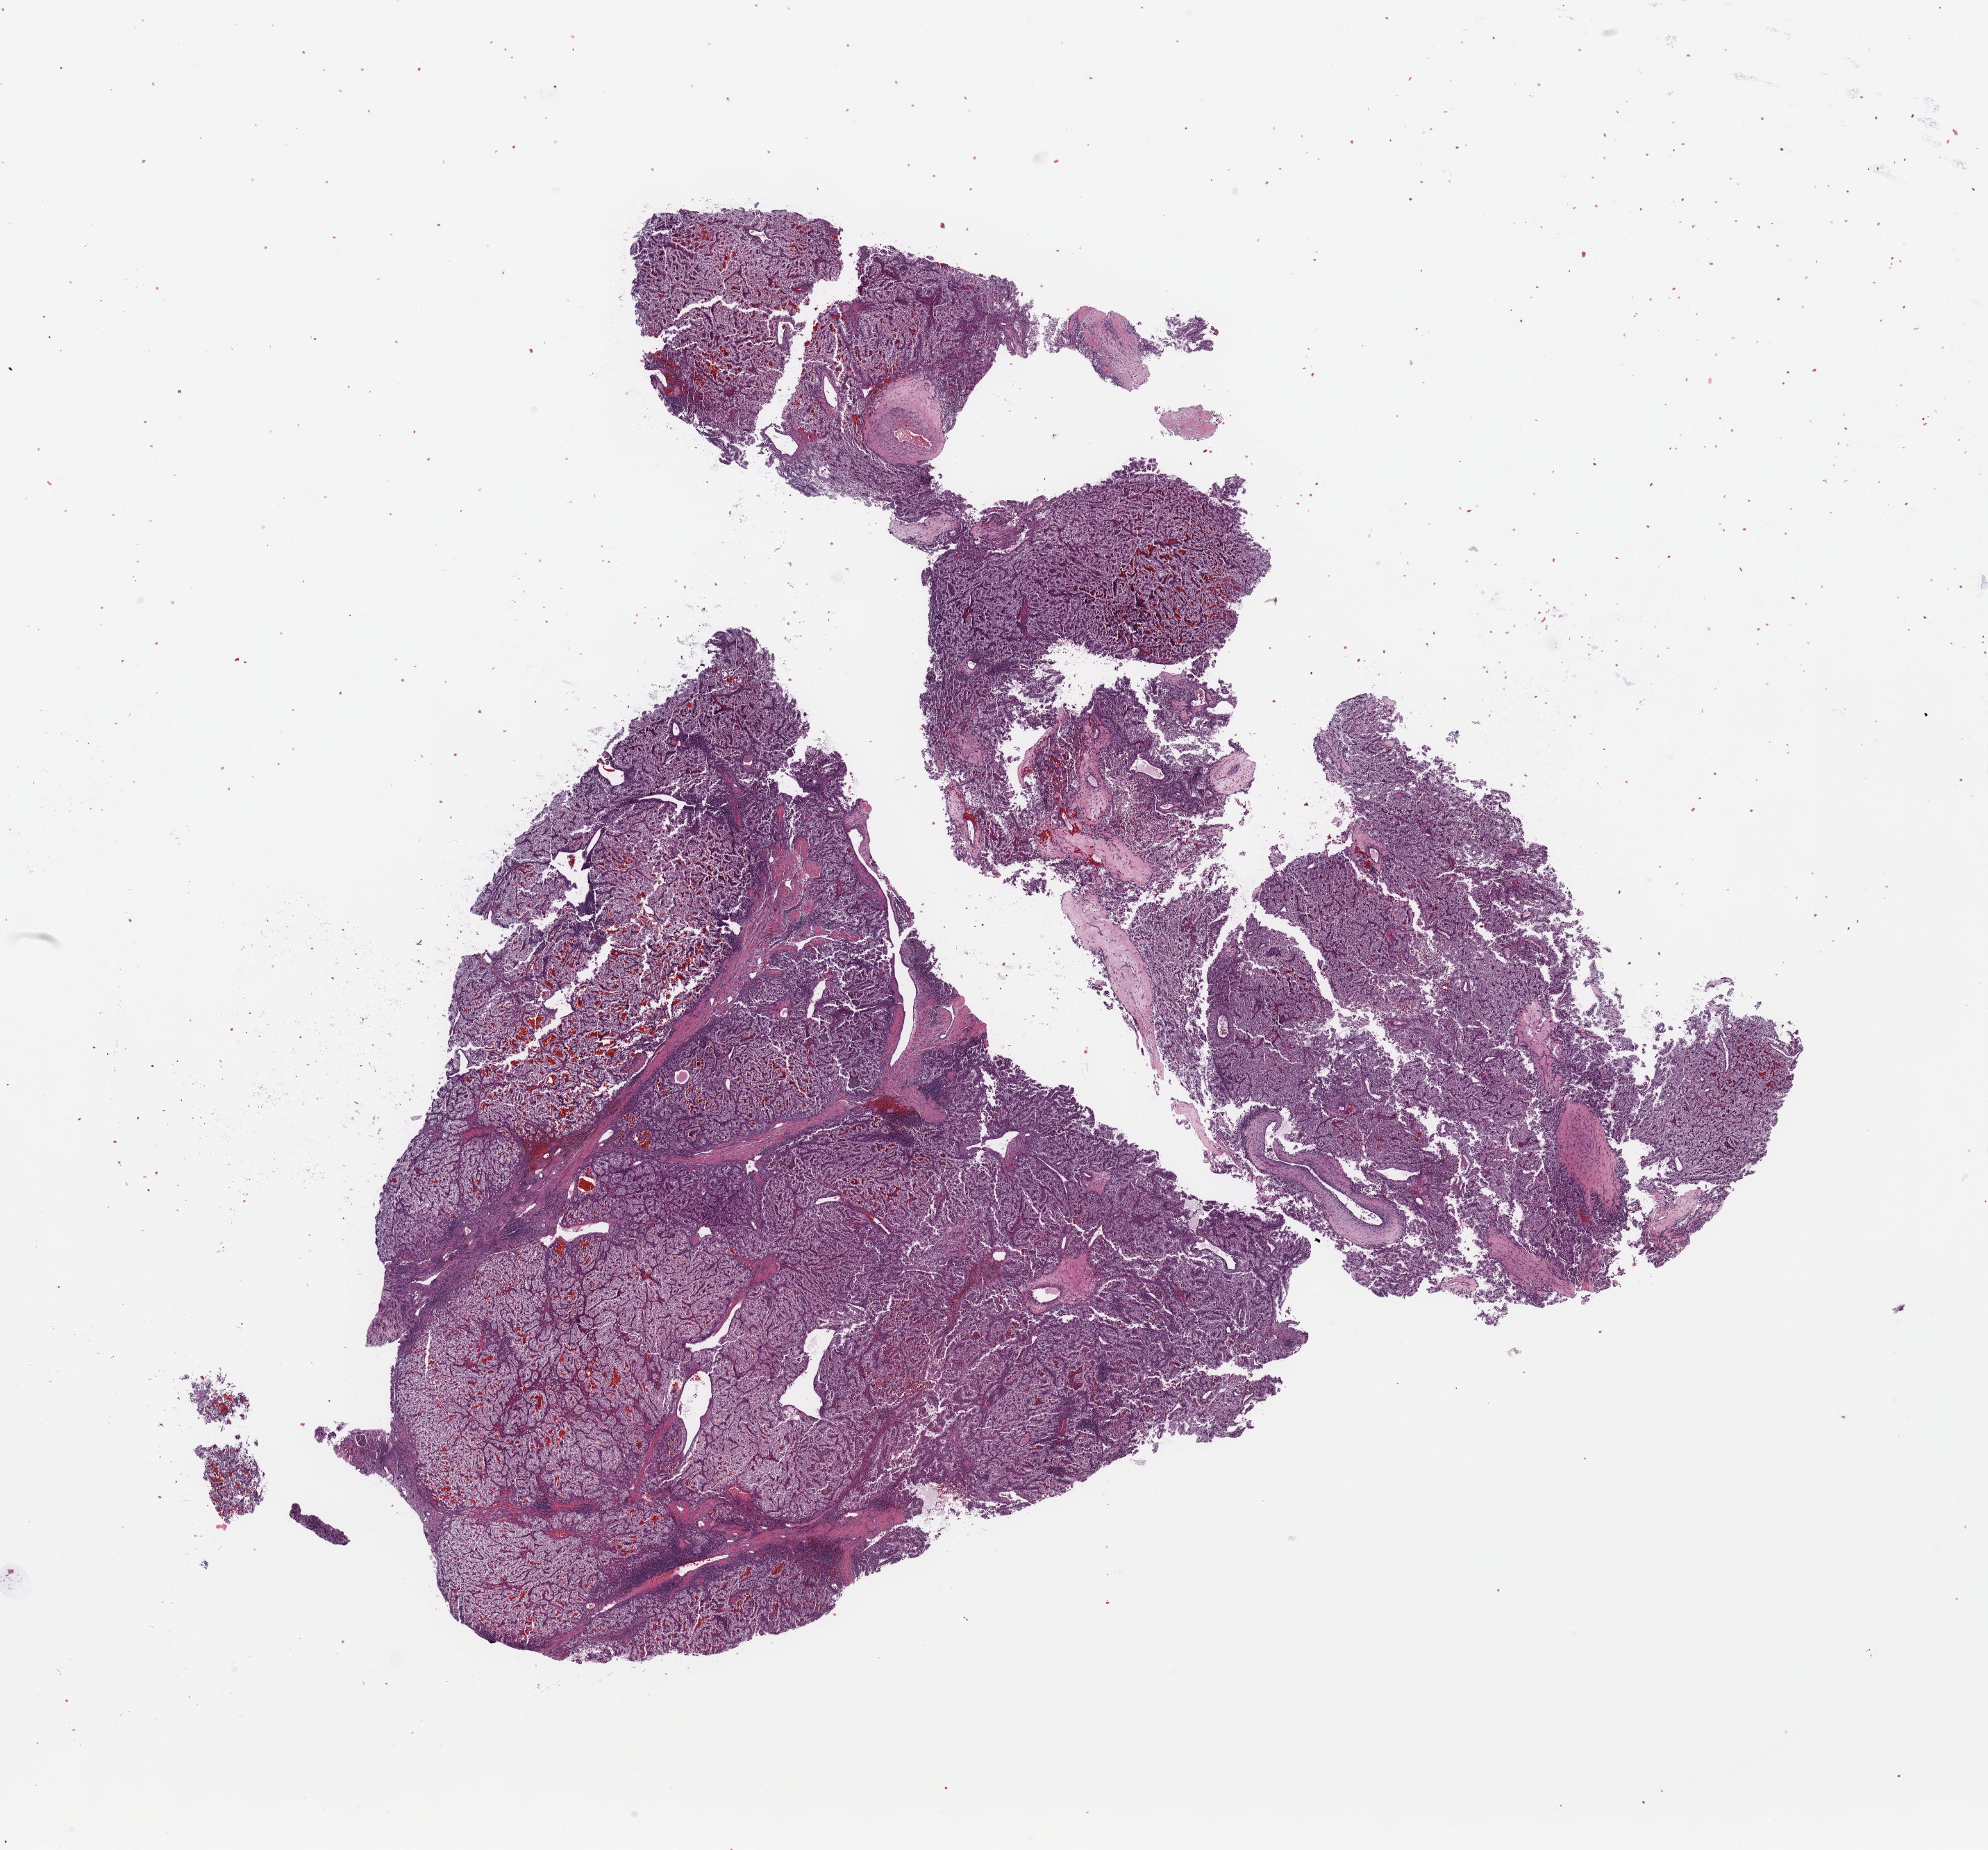
Whole-slide histology image, H&E-stained, shown as a low-resolution overview of the whole scanned area (about 22.6 x 21.1 mm, from a 20x scan); tumour tissue sample, sampled site: kidney. Male, 53 y/o. Histologic grade: G3 (poorly differentiated). Composition of this section per pathologist review: tumour nuclei 85%, necrosis 0%.
• primary tumour site (as recorded): upper pole
• histologic diagnosis: Renal cell carcinoma, NOS